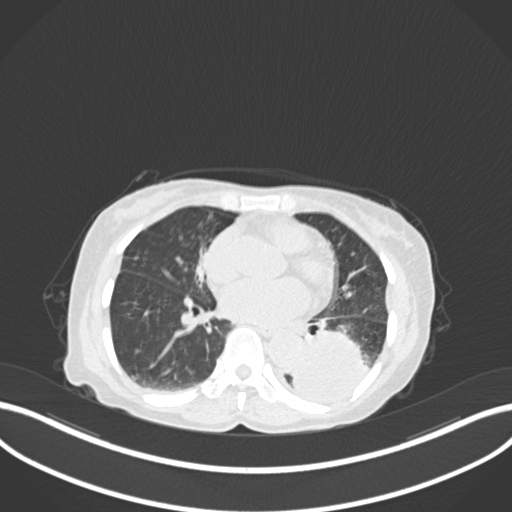
Chest CT, one axial slice; slice 62 of 233 in the series (ordered by position); 120 kVp; lung window (W 1500 / L -600 HU); 512 × 512 image matrix, field of view 400 × 400 mm. Female patient, age 78 years. From the clinical record (not read from this slice): clinical TNM (as recorded): T3 N0 M1.
Outlined on this slice (bounding box drawn by a radiologist):
- lung tumour (recorded histology: squamous cell carcinoma): bounding box [x1, y1, x2, y2] px = [290, 329, 371, 409]